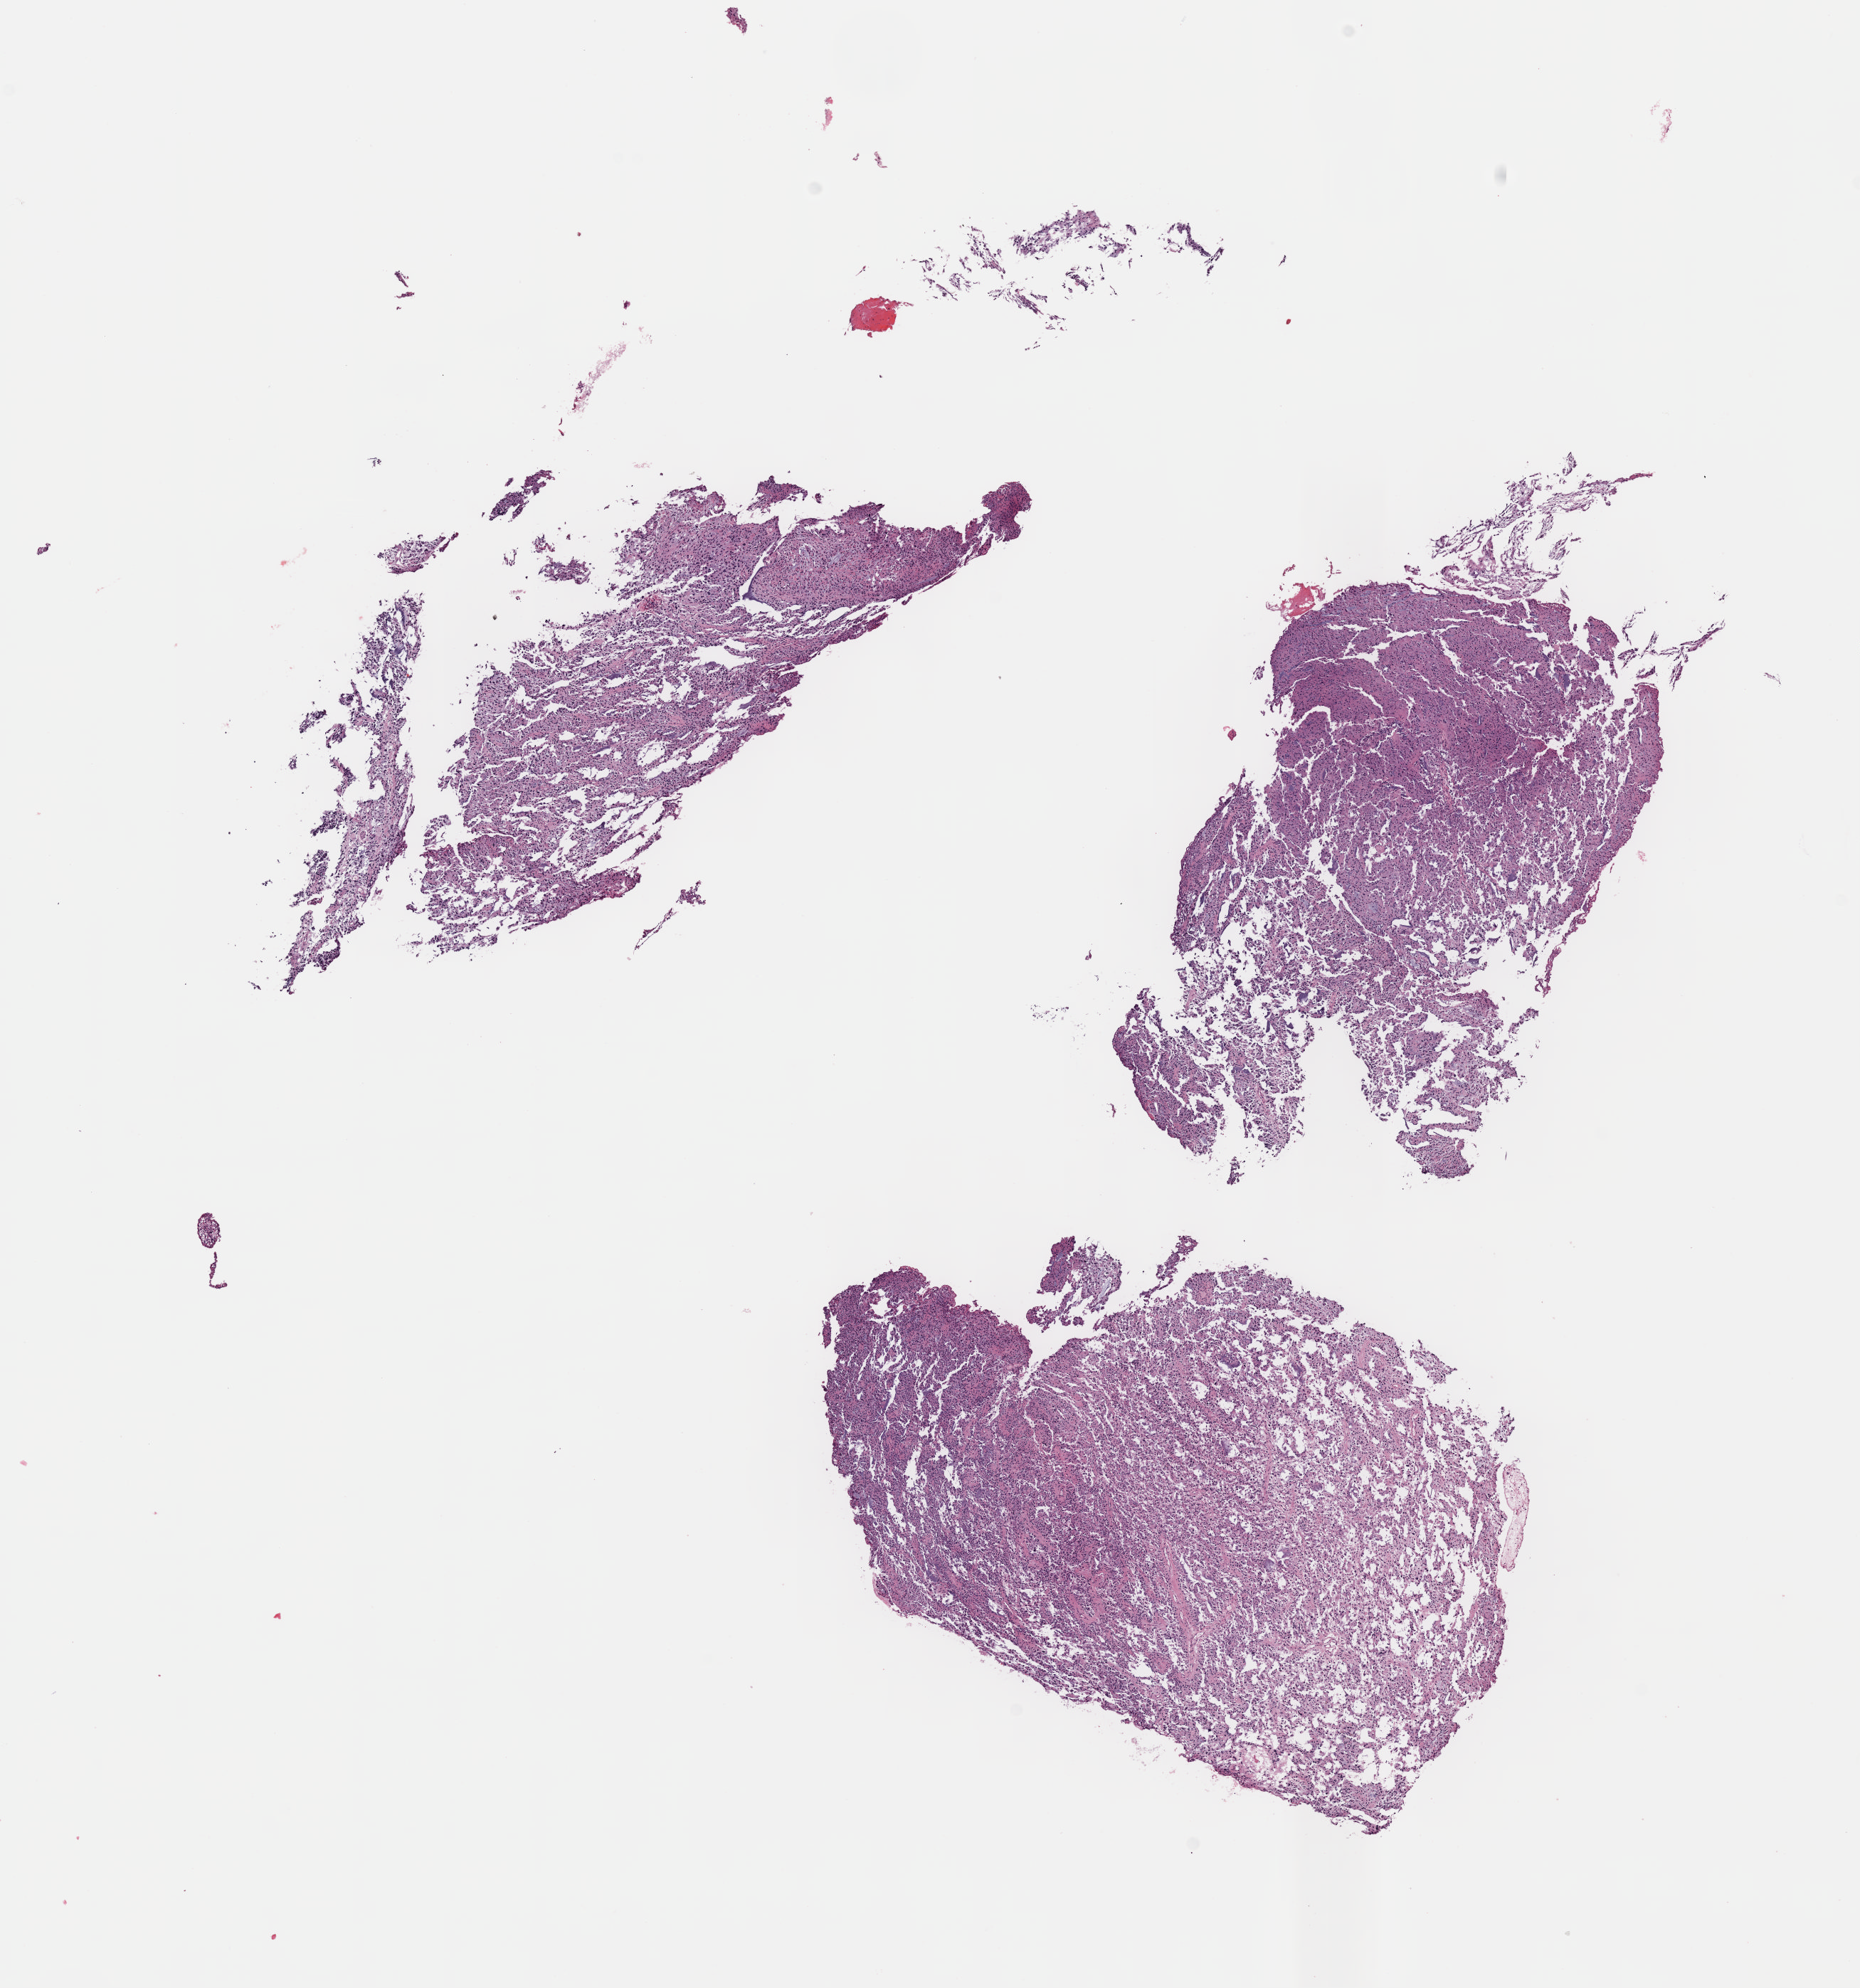
Digitized H&E tissue section (whole slide), low-resolution overview of the scanned area, about 10.6 x 11.3 mm. Formalin-fixed paraffin-embedded (FFPE) diagnostic section. Sample: primary tumour, brain. Patient: male, age at initial diagnosis 50 years. Histologic grade: G2 (moderately differentiated).
Histologic diagnosis: Astrocytoma, NOS (cerebrum).